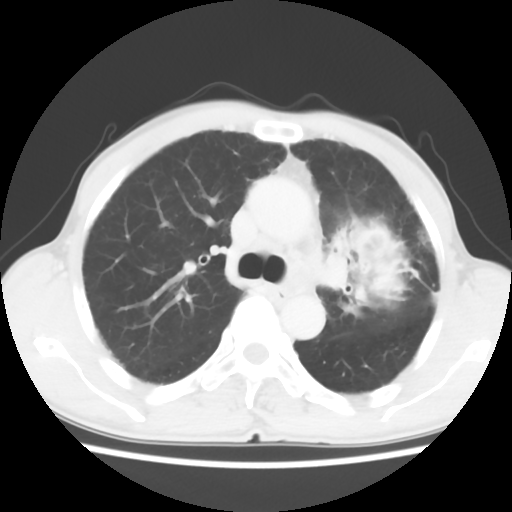
Chest CT, one axial slice. Position 40 of 60 along the scan axis. Reconstruction kernel STANDARD. Lung window (W 1500 / L -600 HU). 5 mm slice thickness. 512 × 512 image matrix, field of view 308 × 308 mm. Male patient, age 64 years. From the clinical record (not read from this slice): clinical TNM (as recorded): T3 N3 M0.
Outlined on this slice (rectangle marked by the reading radiologist):
- lung tumour (recorded histology: adenocarcinoma): box from (x=320, y=212) to (x=423, y=329) px